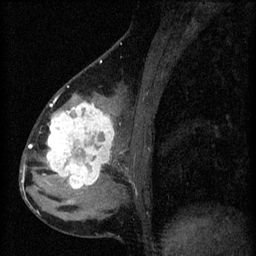
Breast MRI (dynamic contrast-enhanced), one sagittal slice. Position 23 of 60 along the scan axis. 3 images stored at this slice position (order not interpretable as contrast timing). 1.5 T. TE 4.2 ms, TR 8.2 ms. 2 mm slice thickness. 256 × 256 image matrix, field of view 180 × 180 mm. Patient: female, 37 years.
Annotated regions visible in this slice (semi-automatic segmentation, software-assisted and operator-edited):
- analysis volume of interest (the breast-tissue region the enhancement analysis was run in; not a lesion): box from (x=44, y=100) to (x=119, y=197) px
- tumour enhancement mask (voxels above the 70 % enhancement threshold inside the analysis volume of interest): (x=44, y=102)–(x=115, y=189)